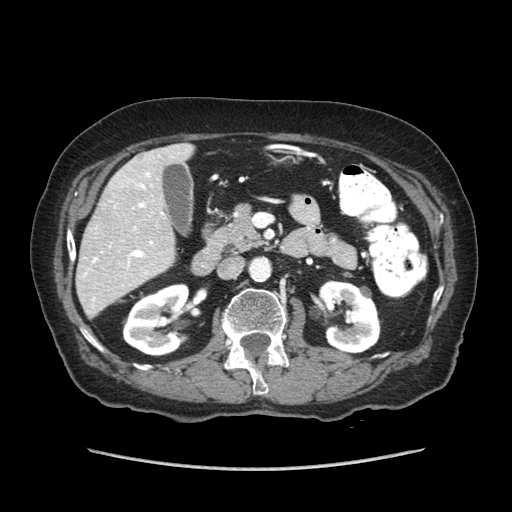
Contrast-enhanced abdominal CT (liver protocol), one axial slice. Position 29 of 89 along the scan axis. Reconstruction kernel STANDARD. 140 kVp. Soft-tissue window (W 400 / L 40 HU). 2.5 mm slice thickness. 512 × 512 image matrix, field of view 360 × 360 mm. From the clinical record (not read from this slice): diagnosis: hepatocellular carcinoma (patient treated with transarterial chemoembolisation; whether this scan precedes or follows treatment is not stated here); TNM stage (as recorded): Stage-IIIA; Child-Pugh class: A; tumour differentiation: well differentiated.
Structures marked on this image (semi-automatic segmentation, software-assisted and operator-edited):
- liver parenchyma outside the tumour (the mass and vessels are separate outlines, so this box may not span the whole liver): bounding box [x1, y1, x2, y2] px = [76, 142, 194, 317]
- mass: [108, 157, 155, 196]
- liver vessels: [84, 172, 163, 301]